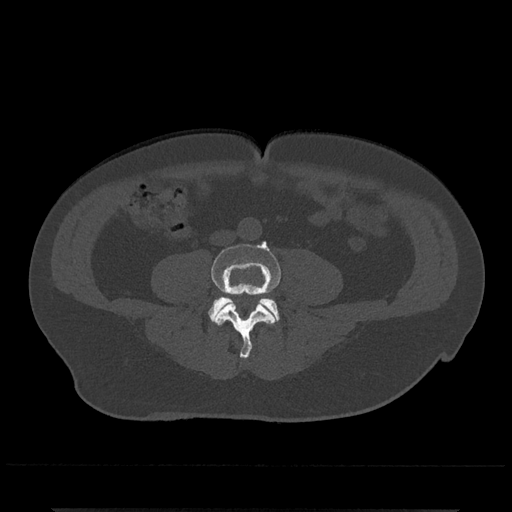
CT including the spine, one axial slice. Slice 134 of 797 in the series (ordered by position). Reconstruction kernel Br40s/3. Bone window (W 1800 / L 400 HU). 0.5 mm slice thickness. 512 × 512 image matrix. Male patient, age 67 years. Case-level facts recorded for this patient, not image findings: primary cancer: prostate.
Outlined on this slice (semi-automatic segmentation, software-assisted and operator-edited):
- L4 vertebra: bounding box <211,241,281,358> (left, top, right, bottom; pixels)
- L5 vertebra: <208,296,280,321>